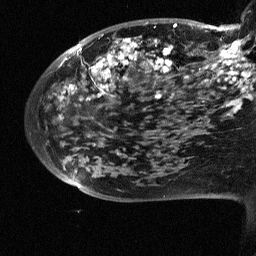
Breast MRI (dynamic contrast-enhanced), one sagittal slice; dynamic contrast-enhanced study with each time point stored as its own series, time point 2 of 3 at this slice position (early post-contrast, ordered by acquisition time); 1.5 T; TE 4.5 ms, TR 11 ms; 2.5 mm slice thickness; 256 × 256 image matrix, field of view 200 × 200 mm. Female patient, age 38 years. From the clinical record (not read from this slice): setting: breast cancer imaged before/during neoadjuvant chemotherapy; receptor status: HR-positive, HER2-negative.
Outlined on this slice (semi-automatic segmentation, software-assisted and operator-edited):
- analysis volume of interest (the breast-tissue region the enhancement analysis was run in; not a lesion): bounding box (x1, y1, x2, y2) in pixels: (88, 18, 252, 126)
- tumour enhancement mask (voxels above the 90 % enhancement threshold inside the analysis volume of interest): (88, 24, 252, 111)